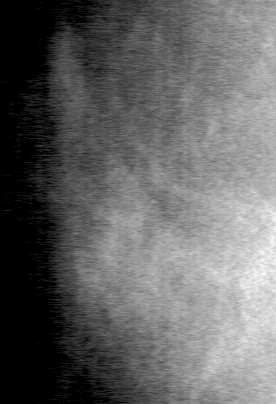
Cropped region of a digitized screen-film mammogram centred on a radiologist-marked abnormality, left breast, MLO view.
Finding: mass, shape irregular, margins ill defined; BI-RADS assessment category 2; subtlety rating 2 on a 1 (subtle) to 5 (obvious) scale; pathology (as recorded): benign.